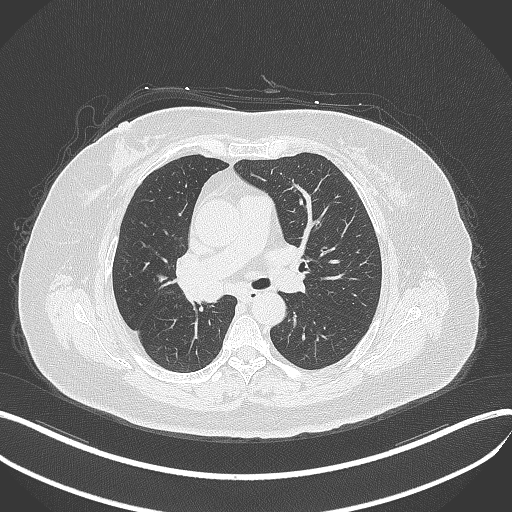
Chest CT, one axial slice; slice 213 of 376 in the series (ordered by position); reconstruction kernel B70f; lung window (W 1500 / L -600 HU); 1 mm slice thickness; 512 × 512 image matrix, field of view 400 × 400 mm. Female patient, age 60 years. Case-level facts recorded for this patient, not image findings: clinical TNM (as recorded): T1c N0 M0; histopathological grade: G1-G2.
Outlined on this slice (bounding box drawn by a radiologist):
- lung tumour (recorded histology: squamous cell carcinoma): box from (x=180, y=277) to (x=229, y=309) px